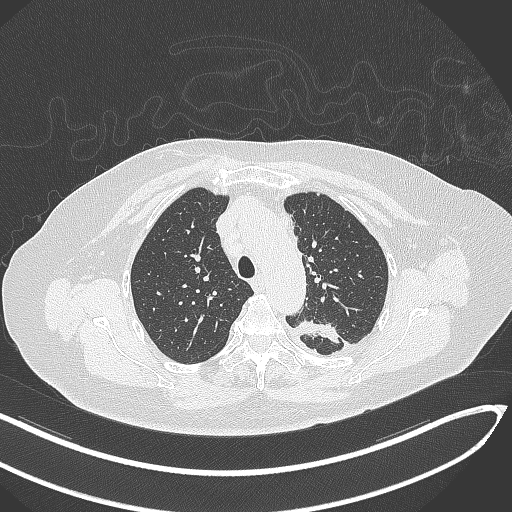
Chest CT, one axial slice; slice 236 of 270 in the series (ordered by position); 120 kVp; lung window (W 1500 / L -600 HU); 1 mm slice thickness; 512 × 512 image matrix, field of view 400 × 400 mm. Female patient, age 76 years. Case-level facts recorded for this patient, not image findings: clinical TNM (as recorded): T1c N0 M0.
Annotated regions visible in this slice (rectangle marked by the reading radiologist):
- lung tumour (recorded histology: adenocarcinoma): bounding box (x1, y1, x2, y2) in pixels: (287, 319, 345, 349)